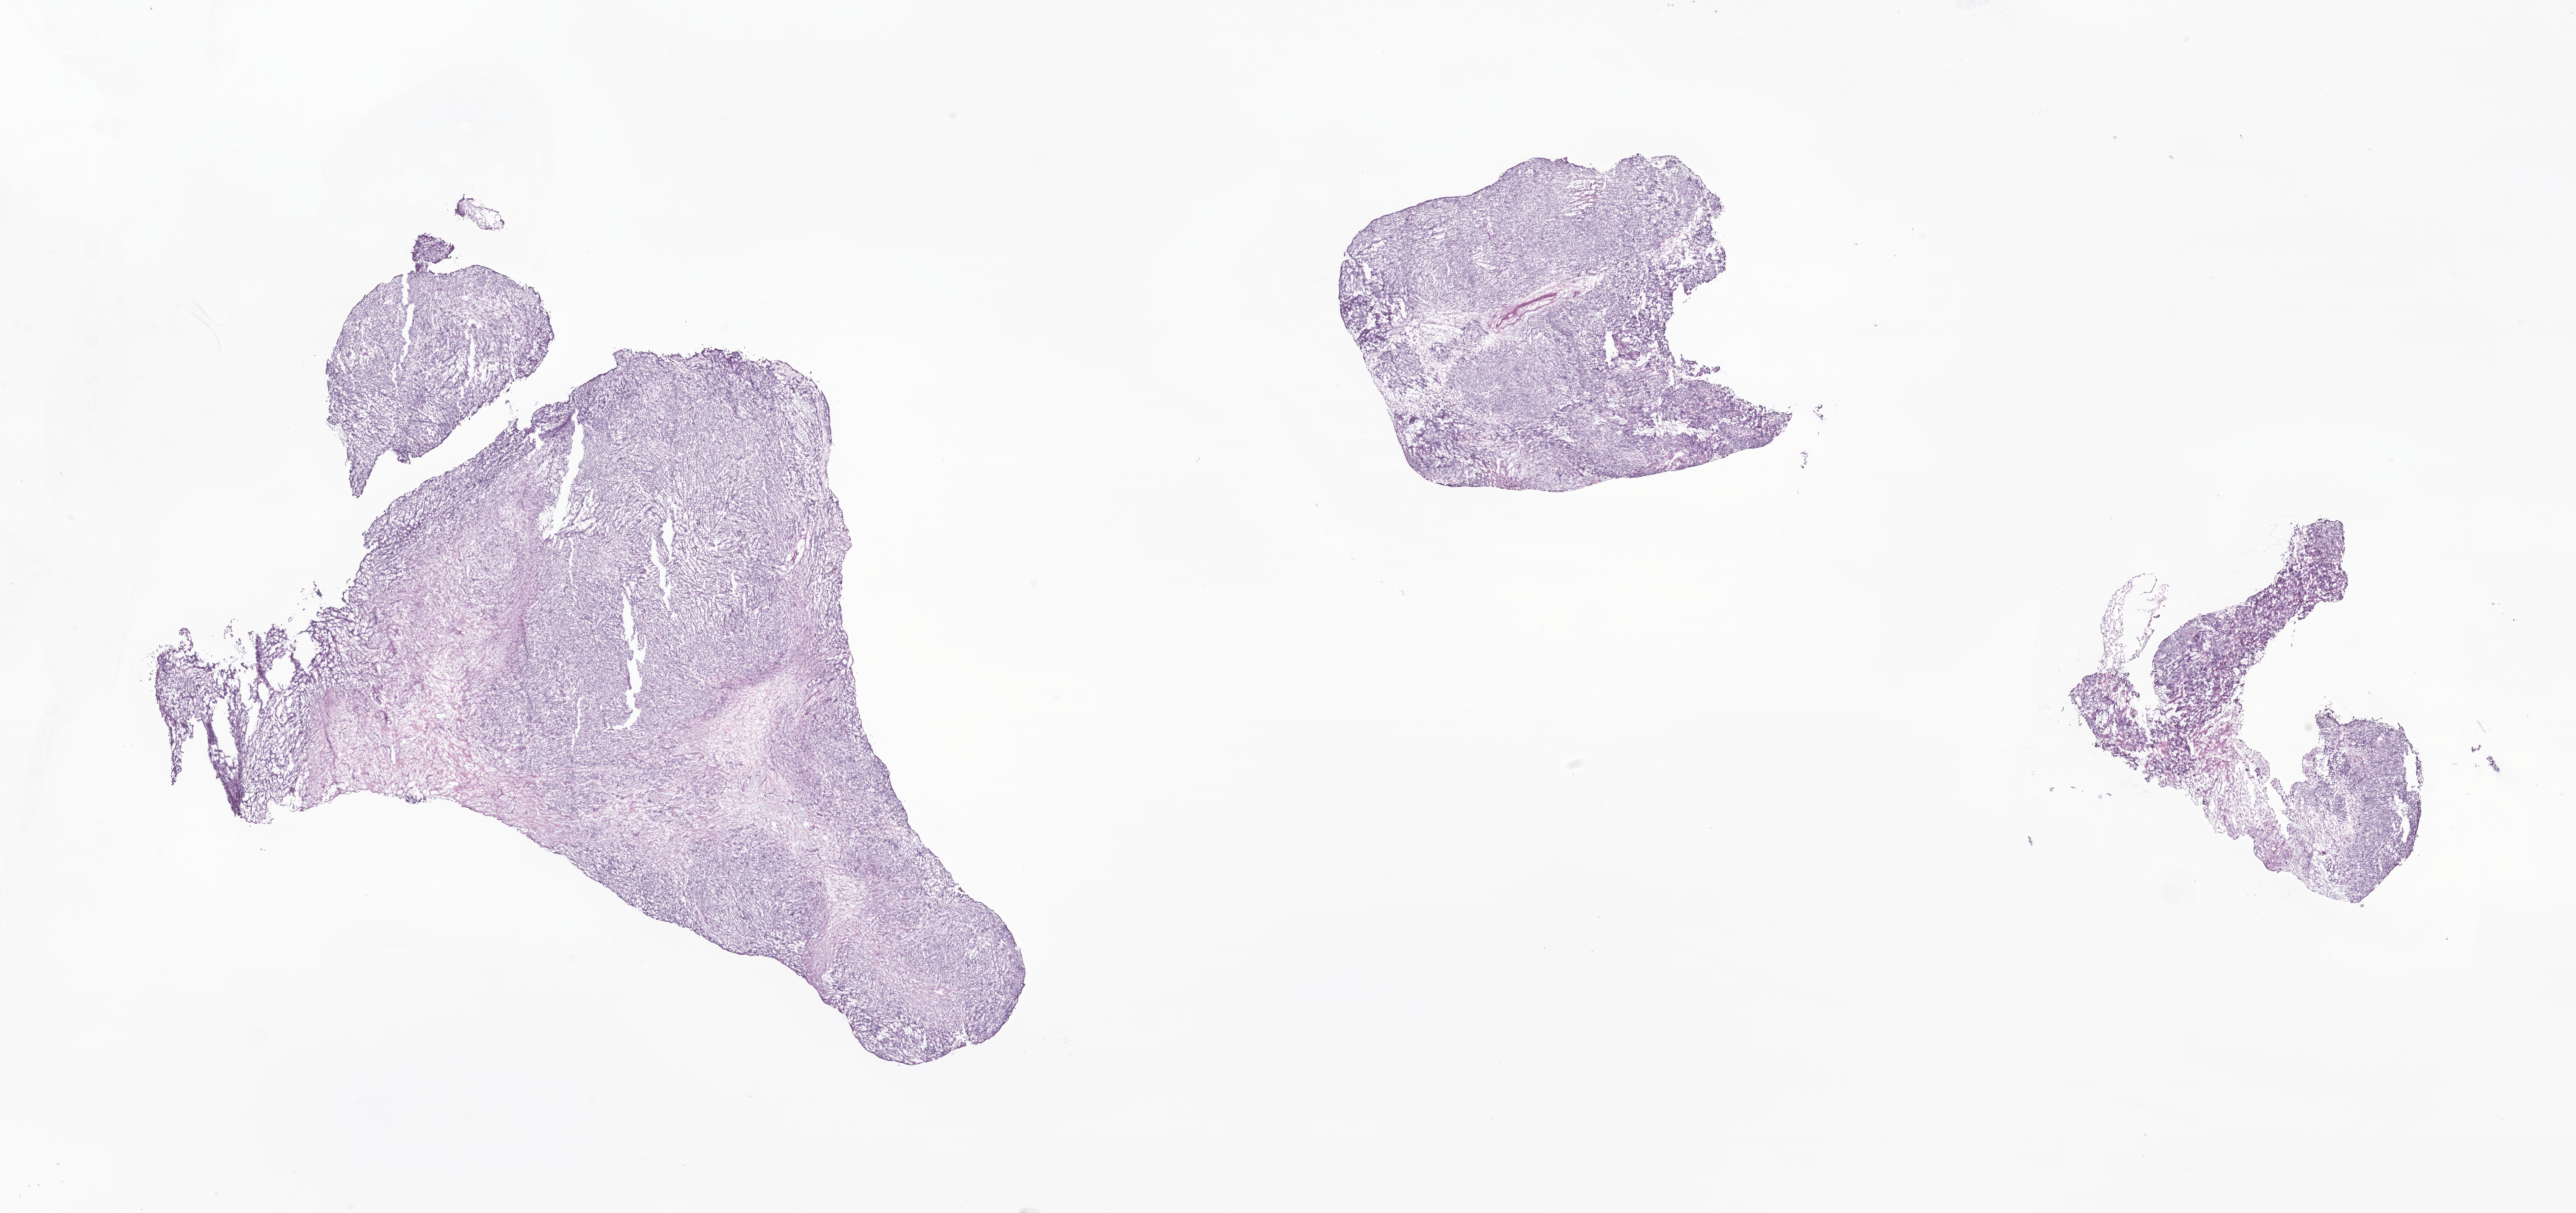
Digitized hematoxylin and eosin (H&E)-stained section of tumor tissue from the retroperitoneum, a low-resolution overview of the entire scanned area, about 32.9 x 15.5 mm, frozen section. Patient: male, age 143 months (11 years 11 months).
Diagnosis (ICD-O-3 morphology term): Neoplasm, uncertain whether benign or malignant.